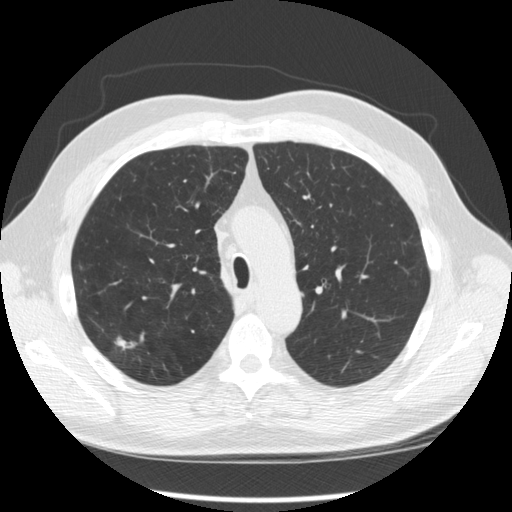
Low-dose screening chest CT, axial slice, second annual screen, lung window (W 1500 / L -600 HU), 2.5 mm slice thickness, slice 80 of 289 in the series. Male participant, aged 64 years at enrolment.
• Expert-annotated lung lesion, bounding box <105,326,150,367> (left, top, right, bottom; pixels).
• The screening reader recorded 3 non-calcified nodules or masses ≥4 mm on this exam (right upper lobe, right upper lobe, right upper lobe); which of them this box marks is not recorded.
• Official screen result: positive, other.
• Lung cancer was diagnosed 411 days after this screen (after the third annual screen): adenocarcinoma, NOS, right upper lobe, moderately differentiated (G2), stage IA (AJCC 6th edition), 14 mm at pathology.